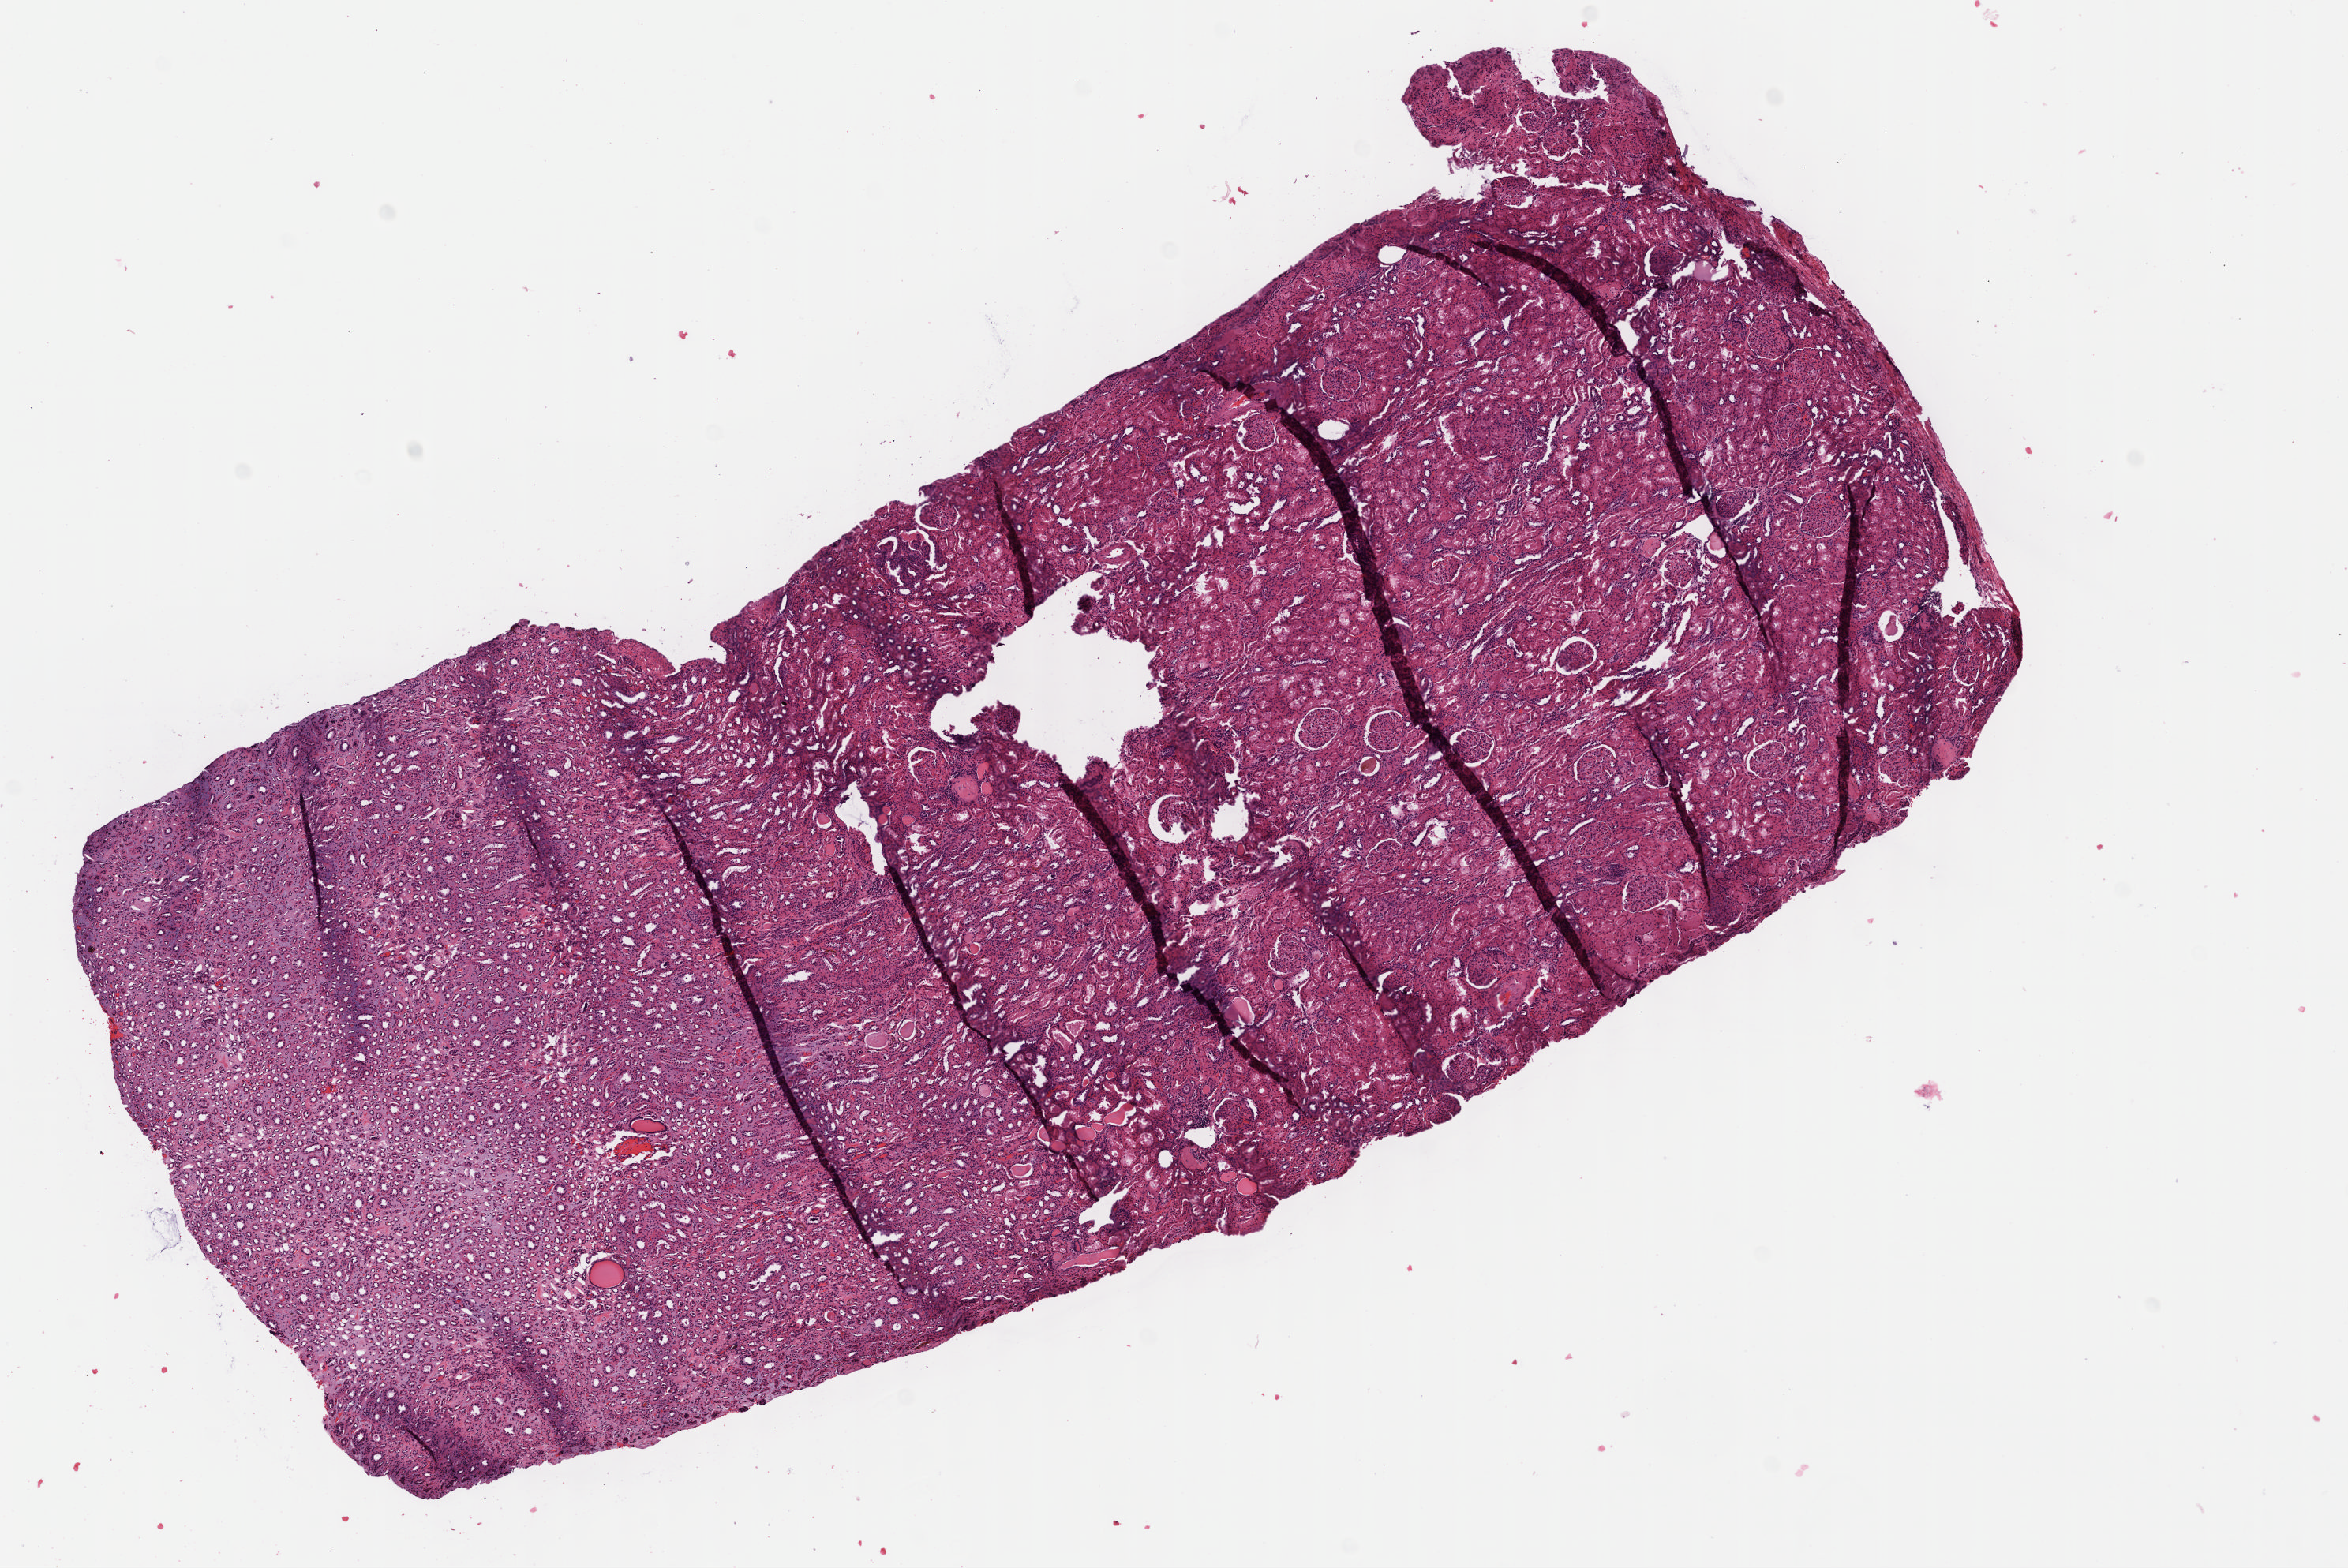
H&E whole-slide image — shown as a low-resolution overview of the whole scanned area (about 11.7 x 7.8 mm). FFPE section. Kidney, primary tumour sample. Female patient; age at initial diagnosis 76 years.
- histologic diagnosis: Renal cell carcinoma, NOS
- AJCC pathologic stage: I